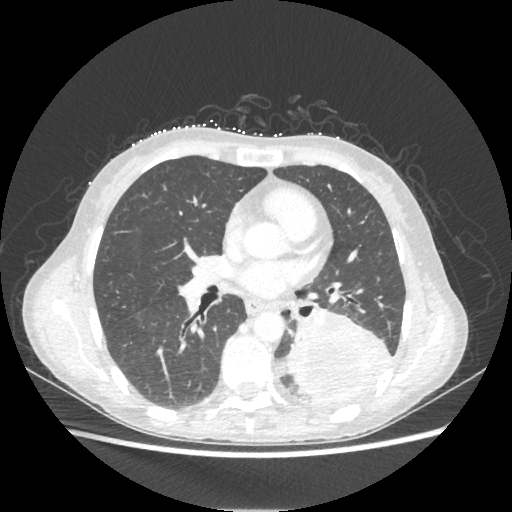
Chest CT, one axial slice; slice 115 of 221 in the series (ordered by position); reconstruction kernel STANDARD; 80 kVp; lung window (W 1500 / L -600 HU); 1.25 mm slice thickness; 512 × 512 image matrix, field of view 360 × 360 mm. Female patient, age 53 years. Case-level facts recorded for this patient, not image findings: clinical TNM (as recorded): T3 N0 M0.
Annotated regions visible in this slice (rectangle marked by the reading radiologist):
- lung tumour (recorded histology: adenocarcinoma): bounding box <287,310,392,402> (left, top, right, bottom; pixels)